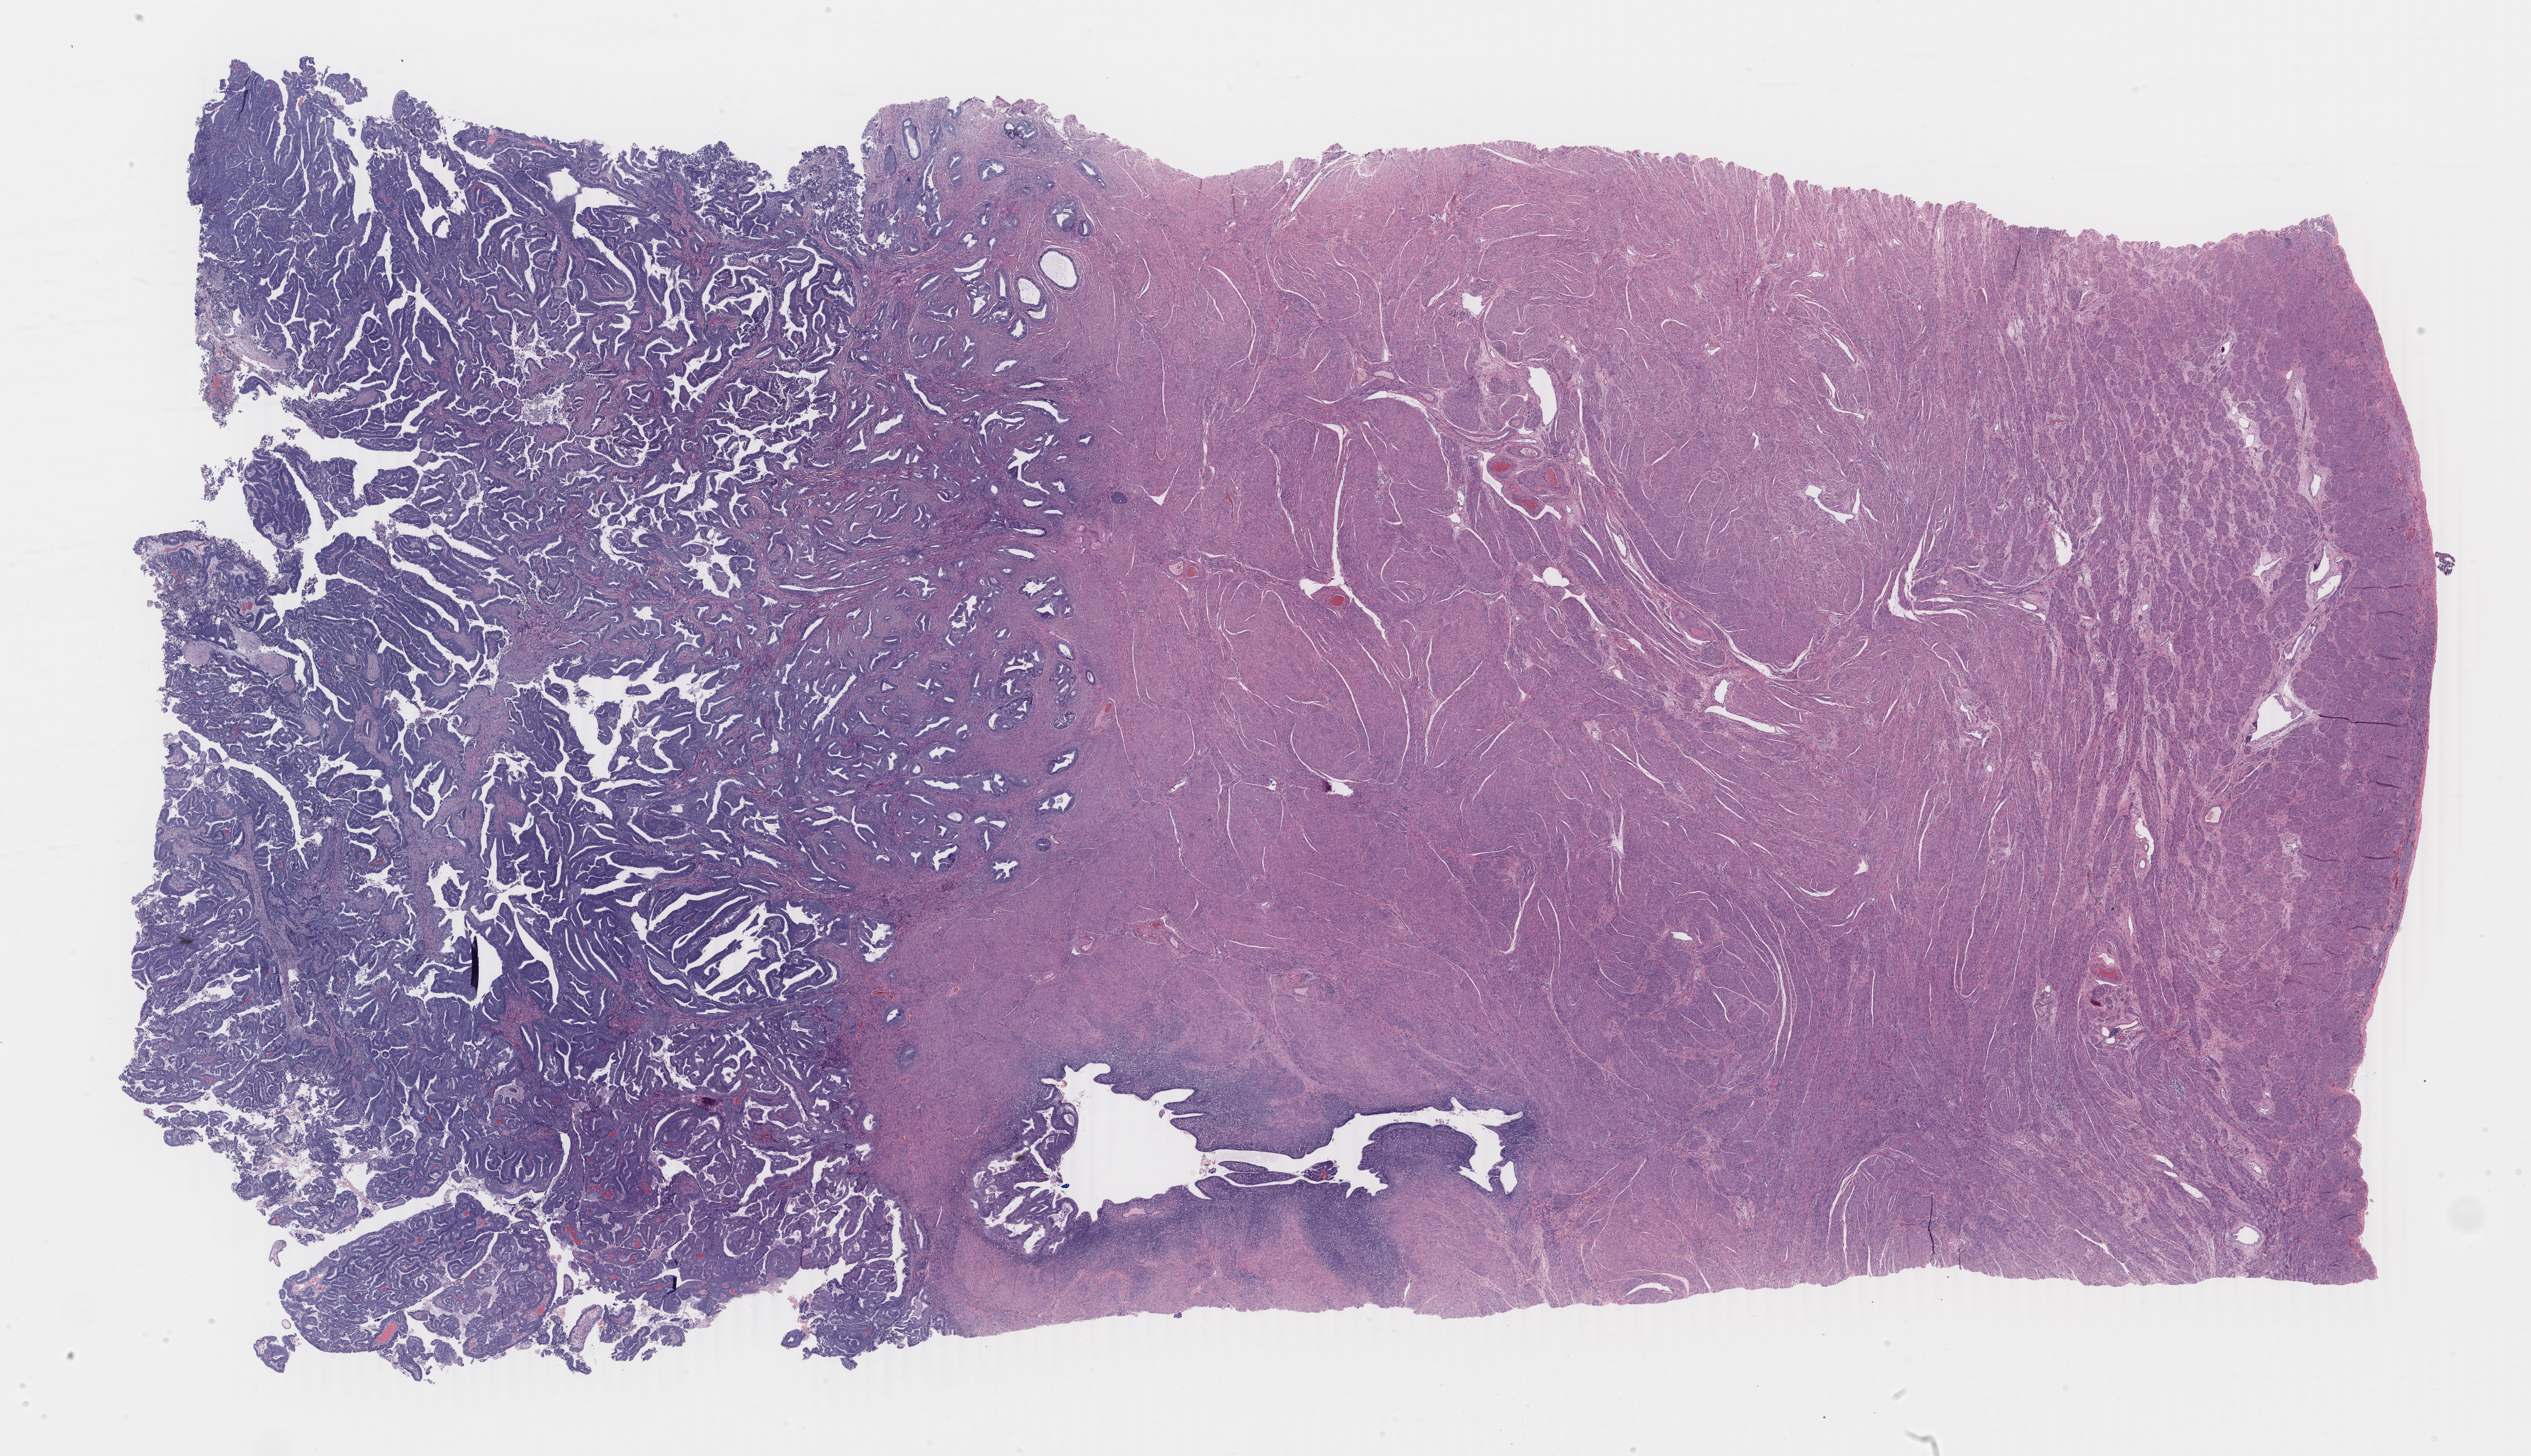
Whole-slide histology image, H&E-stained, whole scanned area (about 32.1 x 18.5 mm, slide scanned at 40x) shown as a low-resolution overview; formalin-fixed paraffin-embedded (FFPE) diagnostic section; primary tumour sample from the uterus. Female patient; age at initial diagnosis 56 years. Histologic grade: G2 (moderately differentiated).
- FIGO stage: IIIA
- diagnosis: Endometrioid adenocarcinoma, NOS (endometrium)